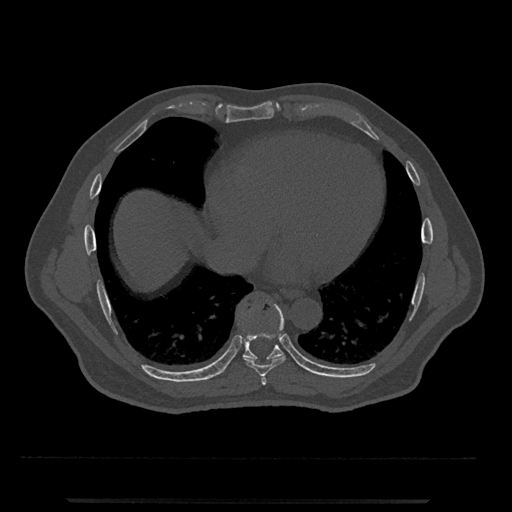
CT including the spine, one axial slice. Slice 604 of 797 in the series (ordered by position). Reconstruction kernel Br40s/3. Bone window (W 1800 / L 400 HU). 0.5 mm slice thickness. 512 × 512 image matrix. Male patient, age 63 years. From the clinical record (not read from this slice): primary cancer: prostate.
Structures marked on this image (semi-automatic segmentation, software-assisted and operator-edited):
- T7 vertebra: box from (x=261, y=376) to (x=267, y=385) px
- T8 vertebra: (x=243, y=304)–(x=286, y=377)
- T9 vertebra: (x=221, y=308)–(x=284, y=374)